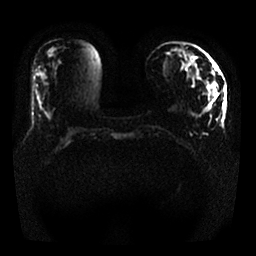
Breast MRI, one axial slice. Slice 4 of 25 in the series (ordered by position). Diffusion-weighted series; image 2 of 4 stored at this slice position (different b-values; order by instance number). 1.5 T. 4 mm slice thickness. 256 × 256 image matrix, field of view 340 × 340 mm. Female patient.
Outlined on this slice (outlined manually by an expert reader):
- tumour on diffusion-weighted imaging: box from (x=208, y=82) to (x=217, y=88) px